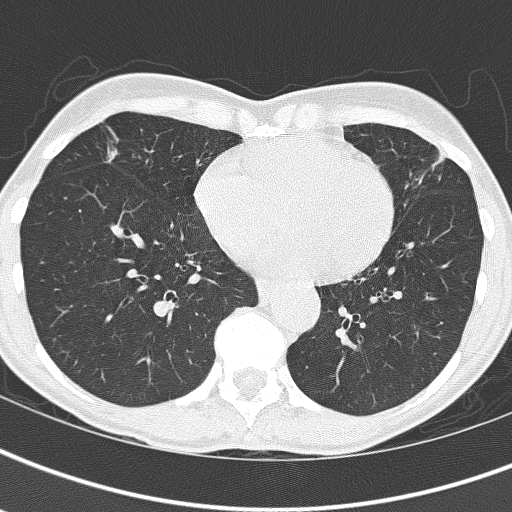
Chest CT (low-dose screening protocol), one axial image. Baseline annual screen. Lung window (W 1500 / L -600 HU). 2 mm slice thickness. Lung (sharp) reconstruction kernel (B60f). Slice 102 of 161 in the series. Female participant, aged 67 years at enrolment. Current smoker at enrolment.
- Expert-annotated lung lesion, bounding box [x1, y1, x2, y2] px = [82, 117, 179, 200].
- Screening reader's record for this exam: no non-calcified nodule ≥4 mm recorded.
- Official screen result: negative screen, significant abnormalities not suspicious for lung cancer.
- Later outcome: lung cancer diagnosed 832 days after this screen — bronchiolo-alveolar adenocarcinoma, NOS, right middle lobe, well differentiated (G1), stage IA (AJCC 6th edition), 25 mm at pathology.